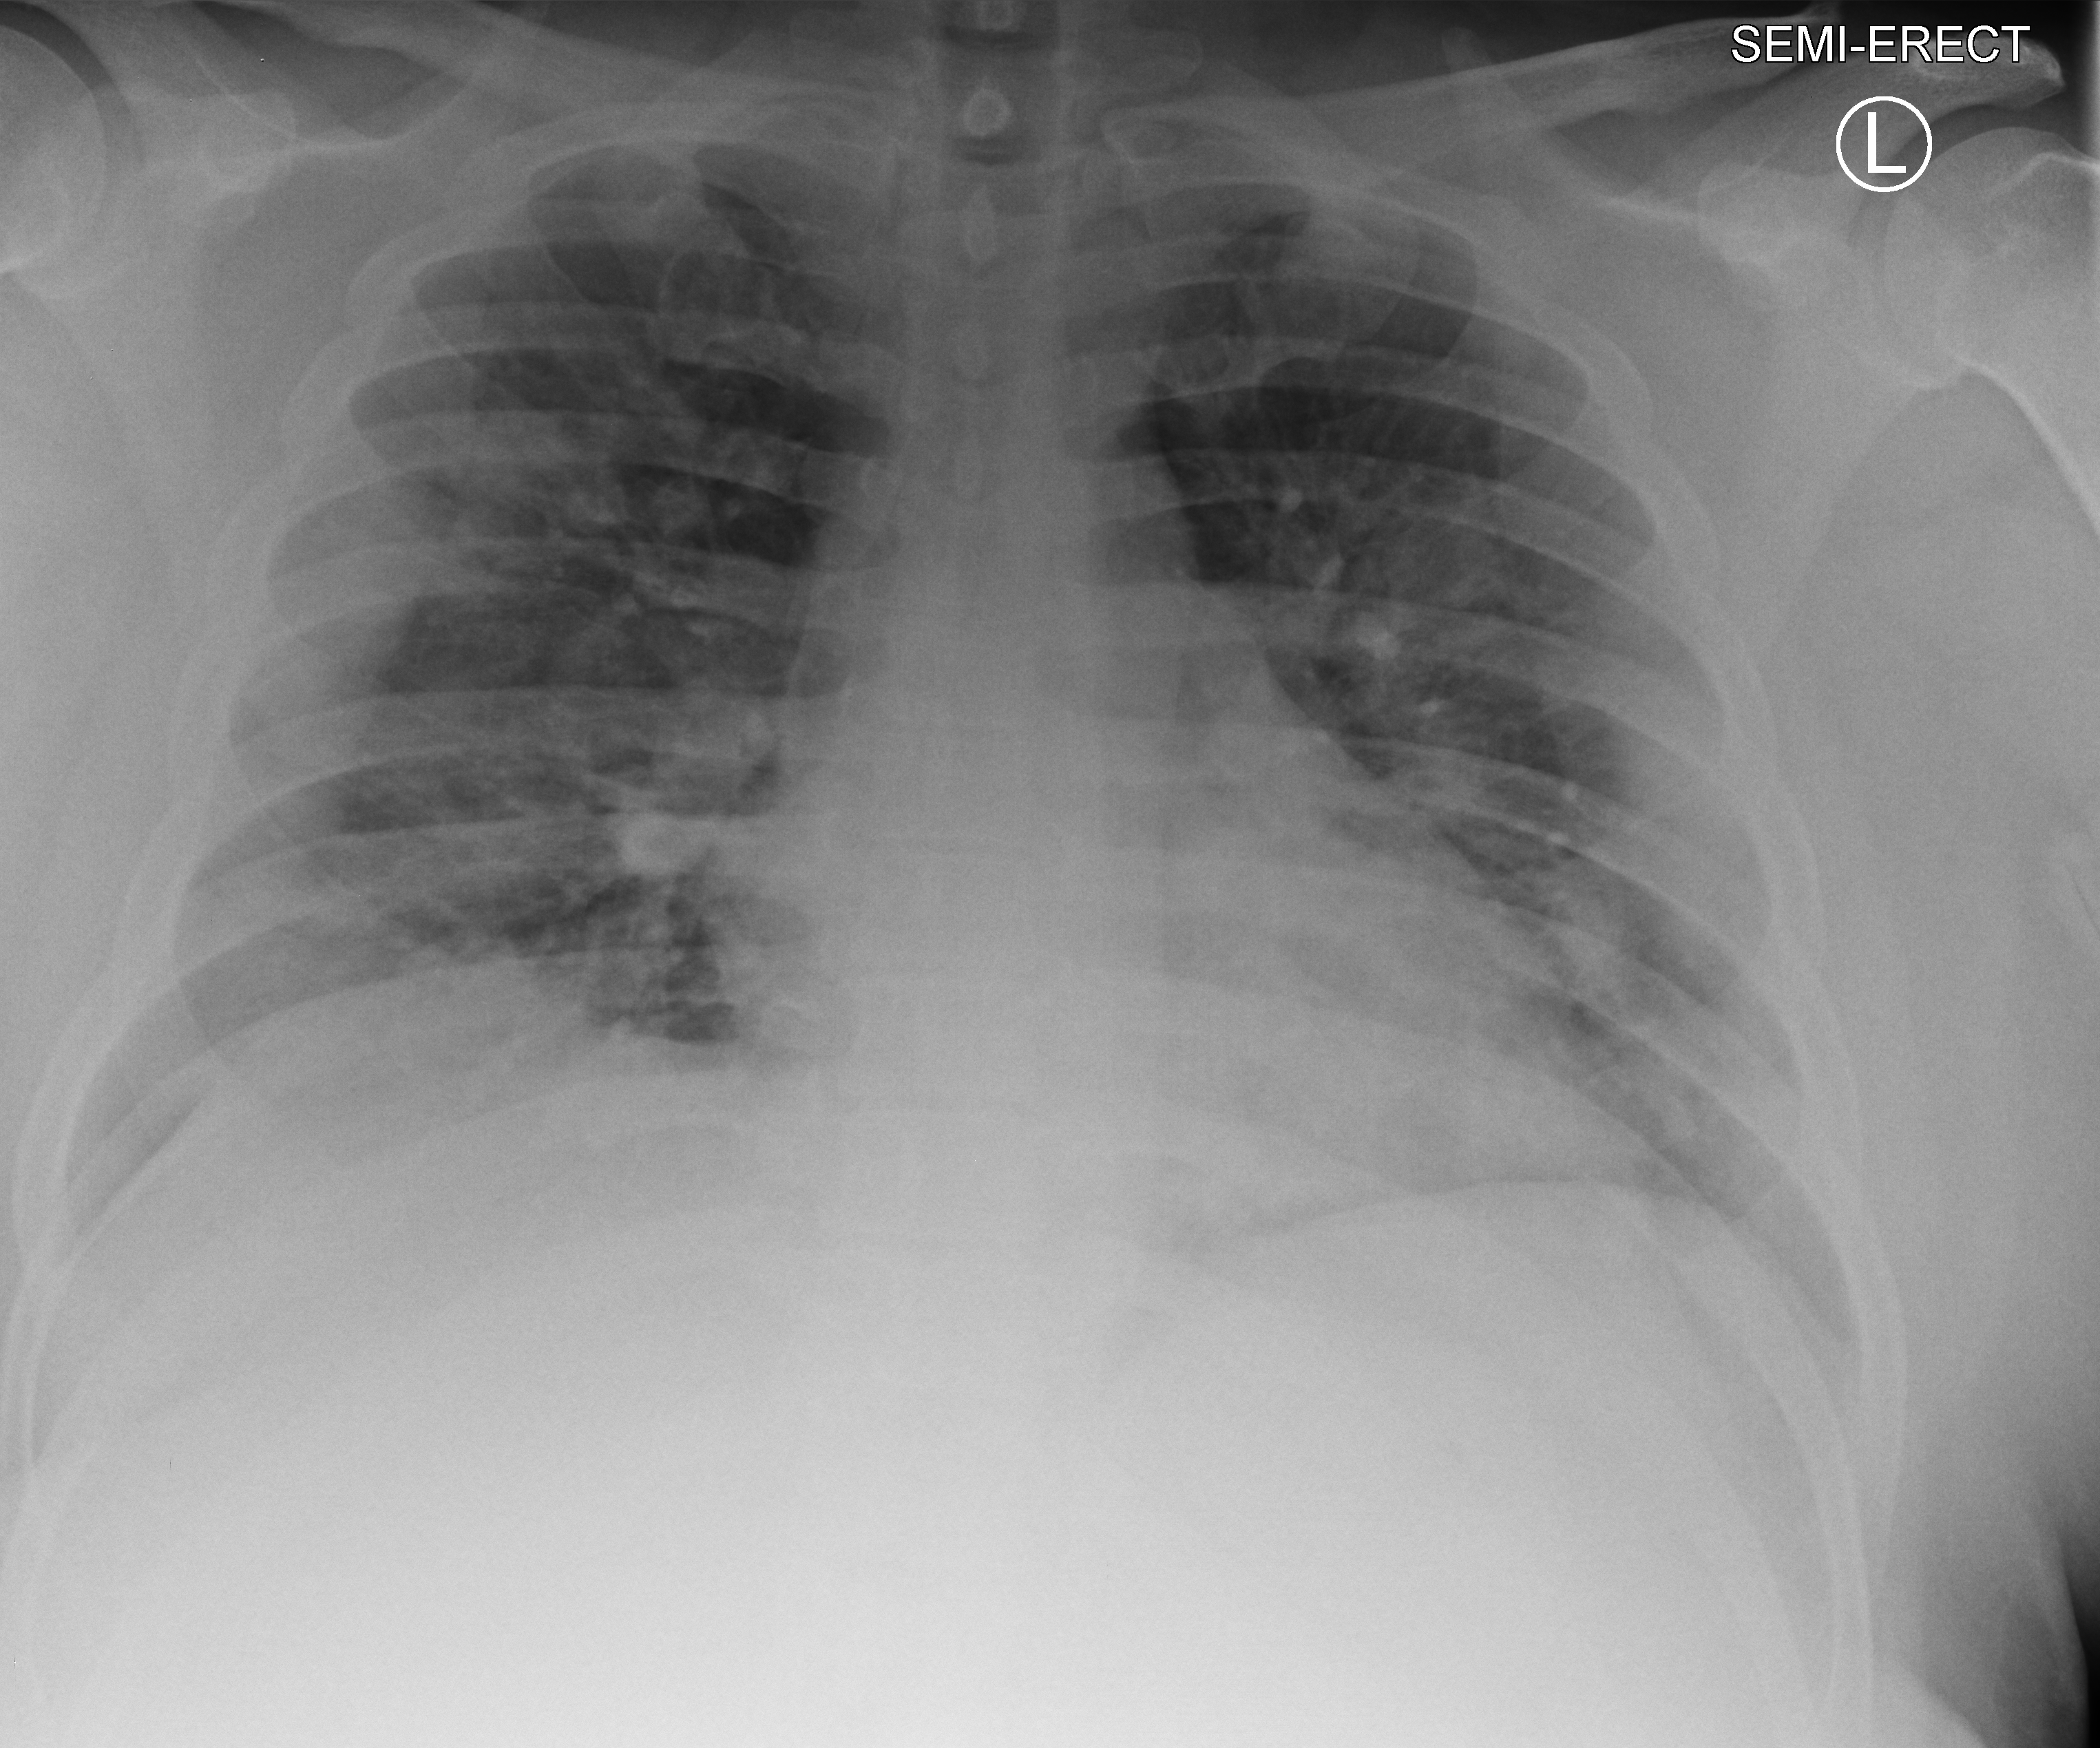
Chest X-ray (portable); anteroposterior (AP) projection. Patient hospitalised with COVID-19; male, aged 18–59 years.
From the hospital-stay record, not from the radiograph (when in the stay this image was taken is not recorded): admitted to intensive care during this hospital stay: no; mechanically ventilated during this hospital stay: no; length of hospital stay: 1 day.